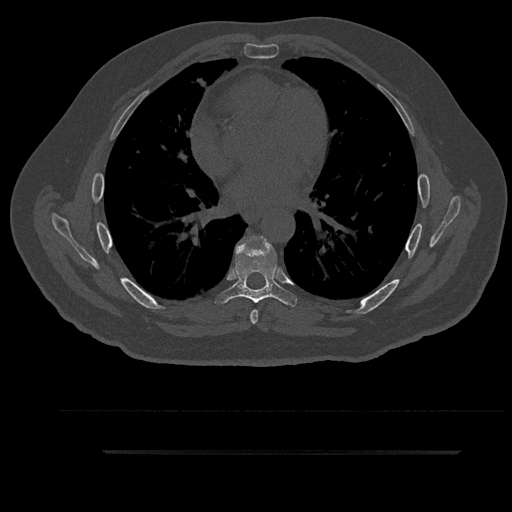
CT including the spine, one axial slice. Slice 539 of 797 in the series (ordered by position). Reconstruction kernel Br40s/3. 120 kVp. Bone window (W 1800 / L 400 HU). 0.5 mm slice thickness. 512 × 512 image matrix. Patient: male, 63 years. From the clinical record (not read from this slice): primary cancer: renal.
Outlined on this slice (semi-automatic segmentation, software-assisted and operator-edited):
- T6 vertebra: bounding box (x1, y1, x2, y2) in pixels: (249, 236, 263, 324)
- T7 vertebra: (215, 237, 298, 307)